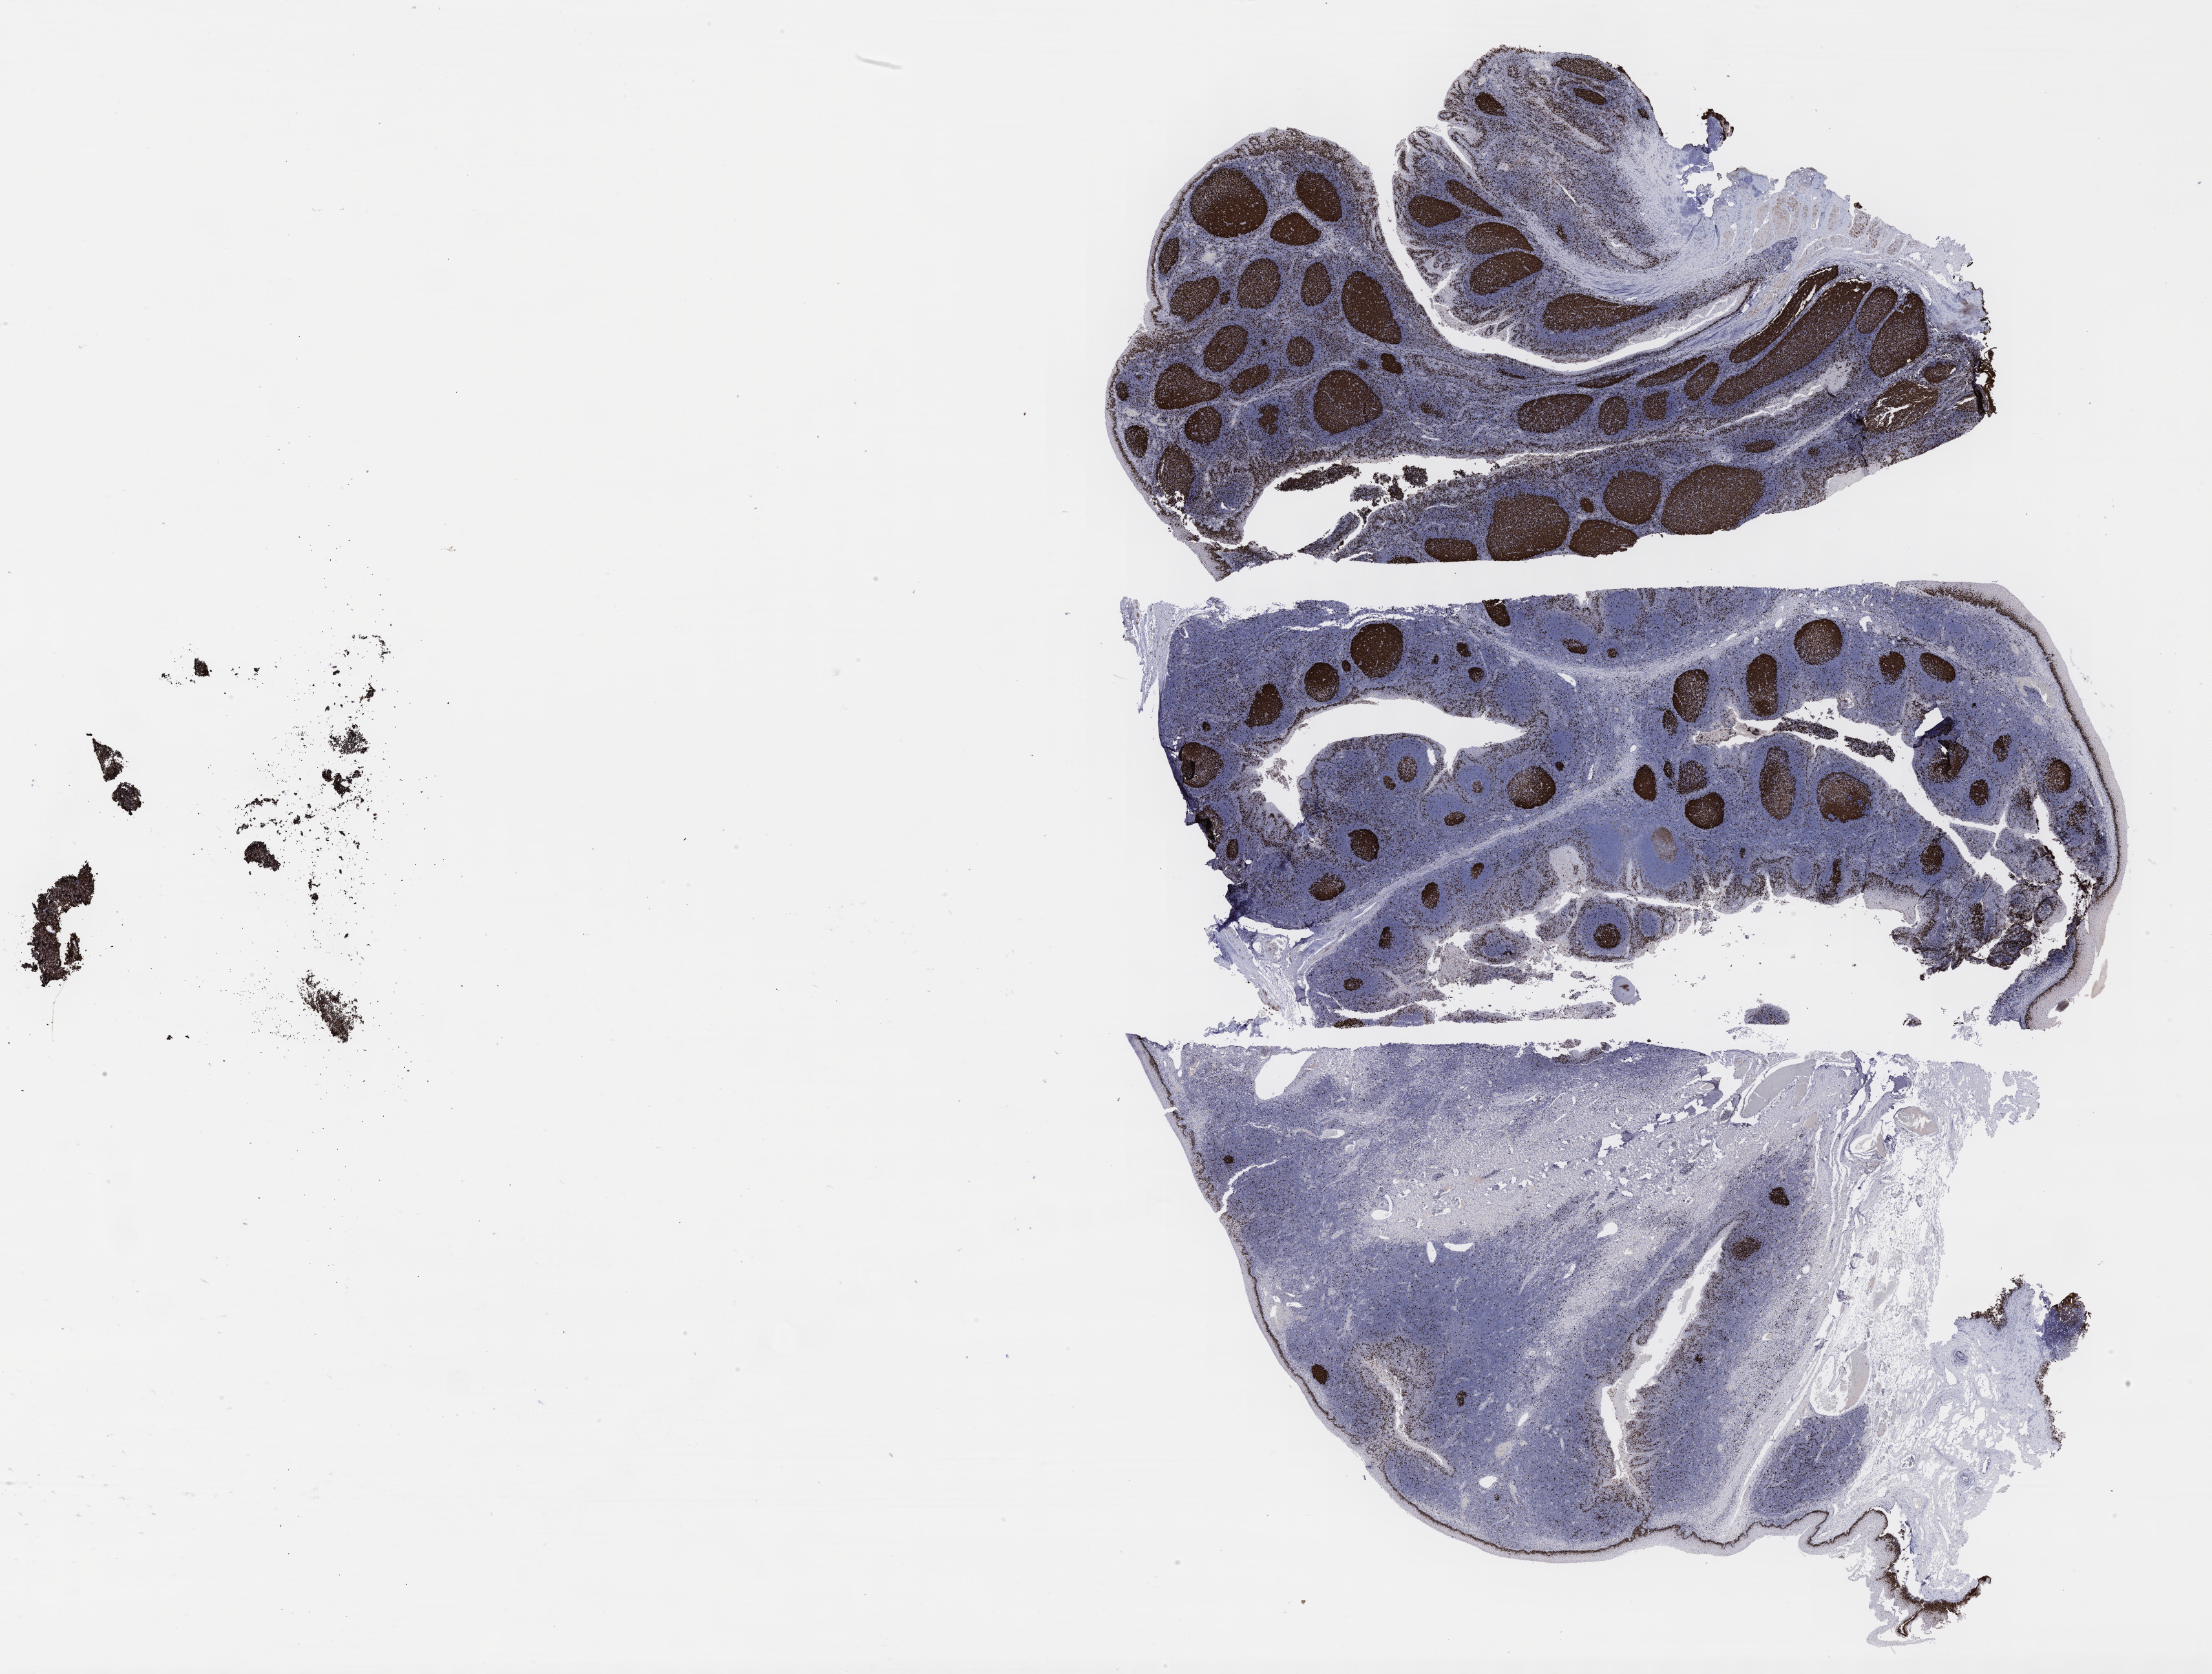
IHC for Ki-67, whole-slide image — whole scanned area (about 27.7 x 20.9 mm) shown as a low-resolution overview. Tumor tissue. Anatomic site: peritoneum. Patient: female, age at initial diagnosis 6 years.
Diagnosis: Burkitt lymphoma, NOS.